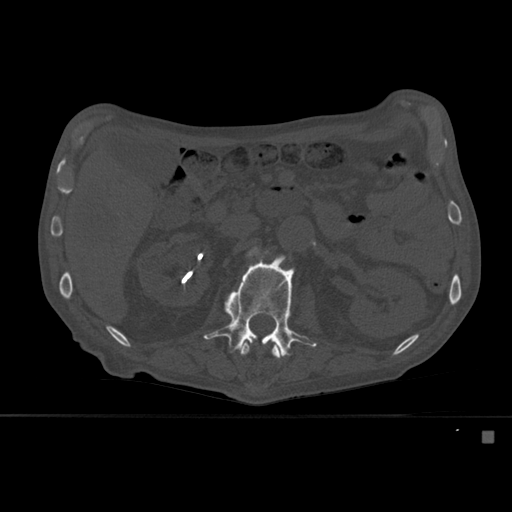
CT including the spine, one axial slice. Slice 239 of 527 in the series (ordered by position). Bone window (W 1800 / L 400 HU). 1.5 mm slice thickness. 512 × 512 image matrix. Patient: male, 78 years. From the clinical record (not read from this slice): primary cancer: prostate.
Structures marked on this image (semi-automatic segmentation, software-assisted and operator-edited):
- L1 vertebra: bounding box (x1, y1, x2, y2) in pixels: (239, 342, 282, 359)
- L2 vertebra: (204, 256, 317, 357)